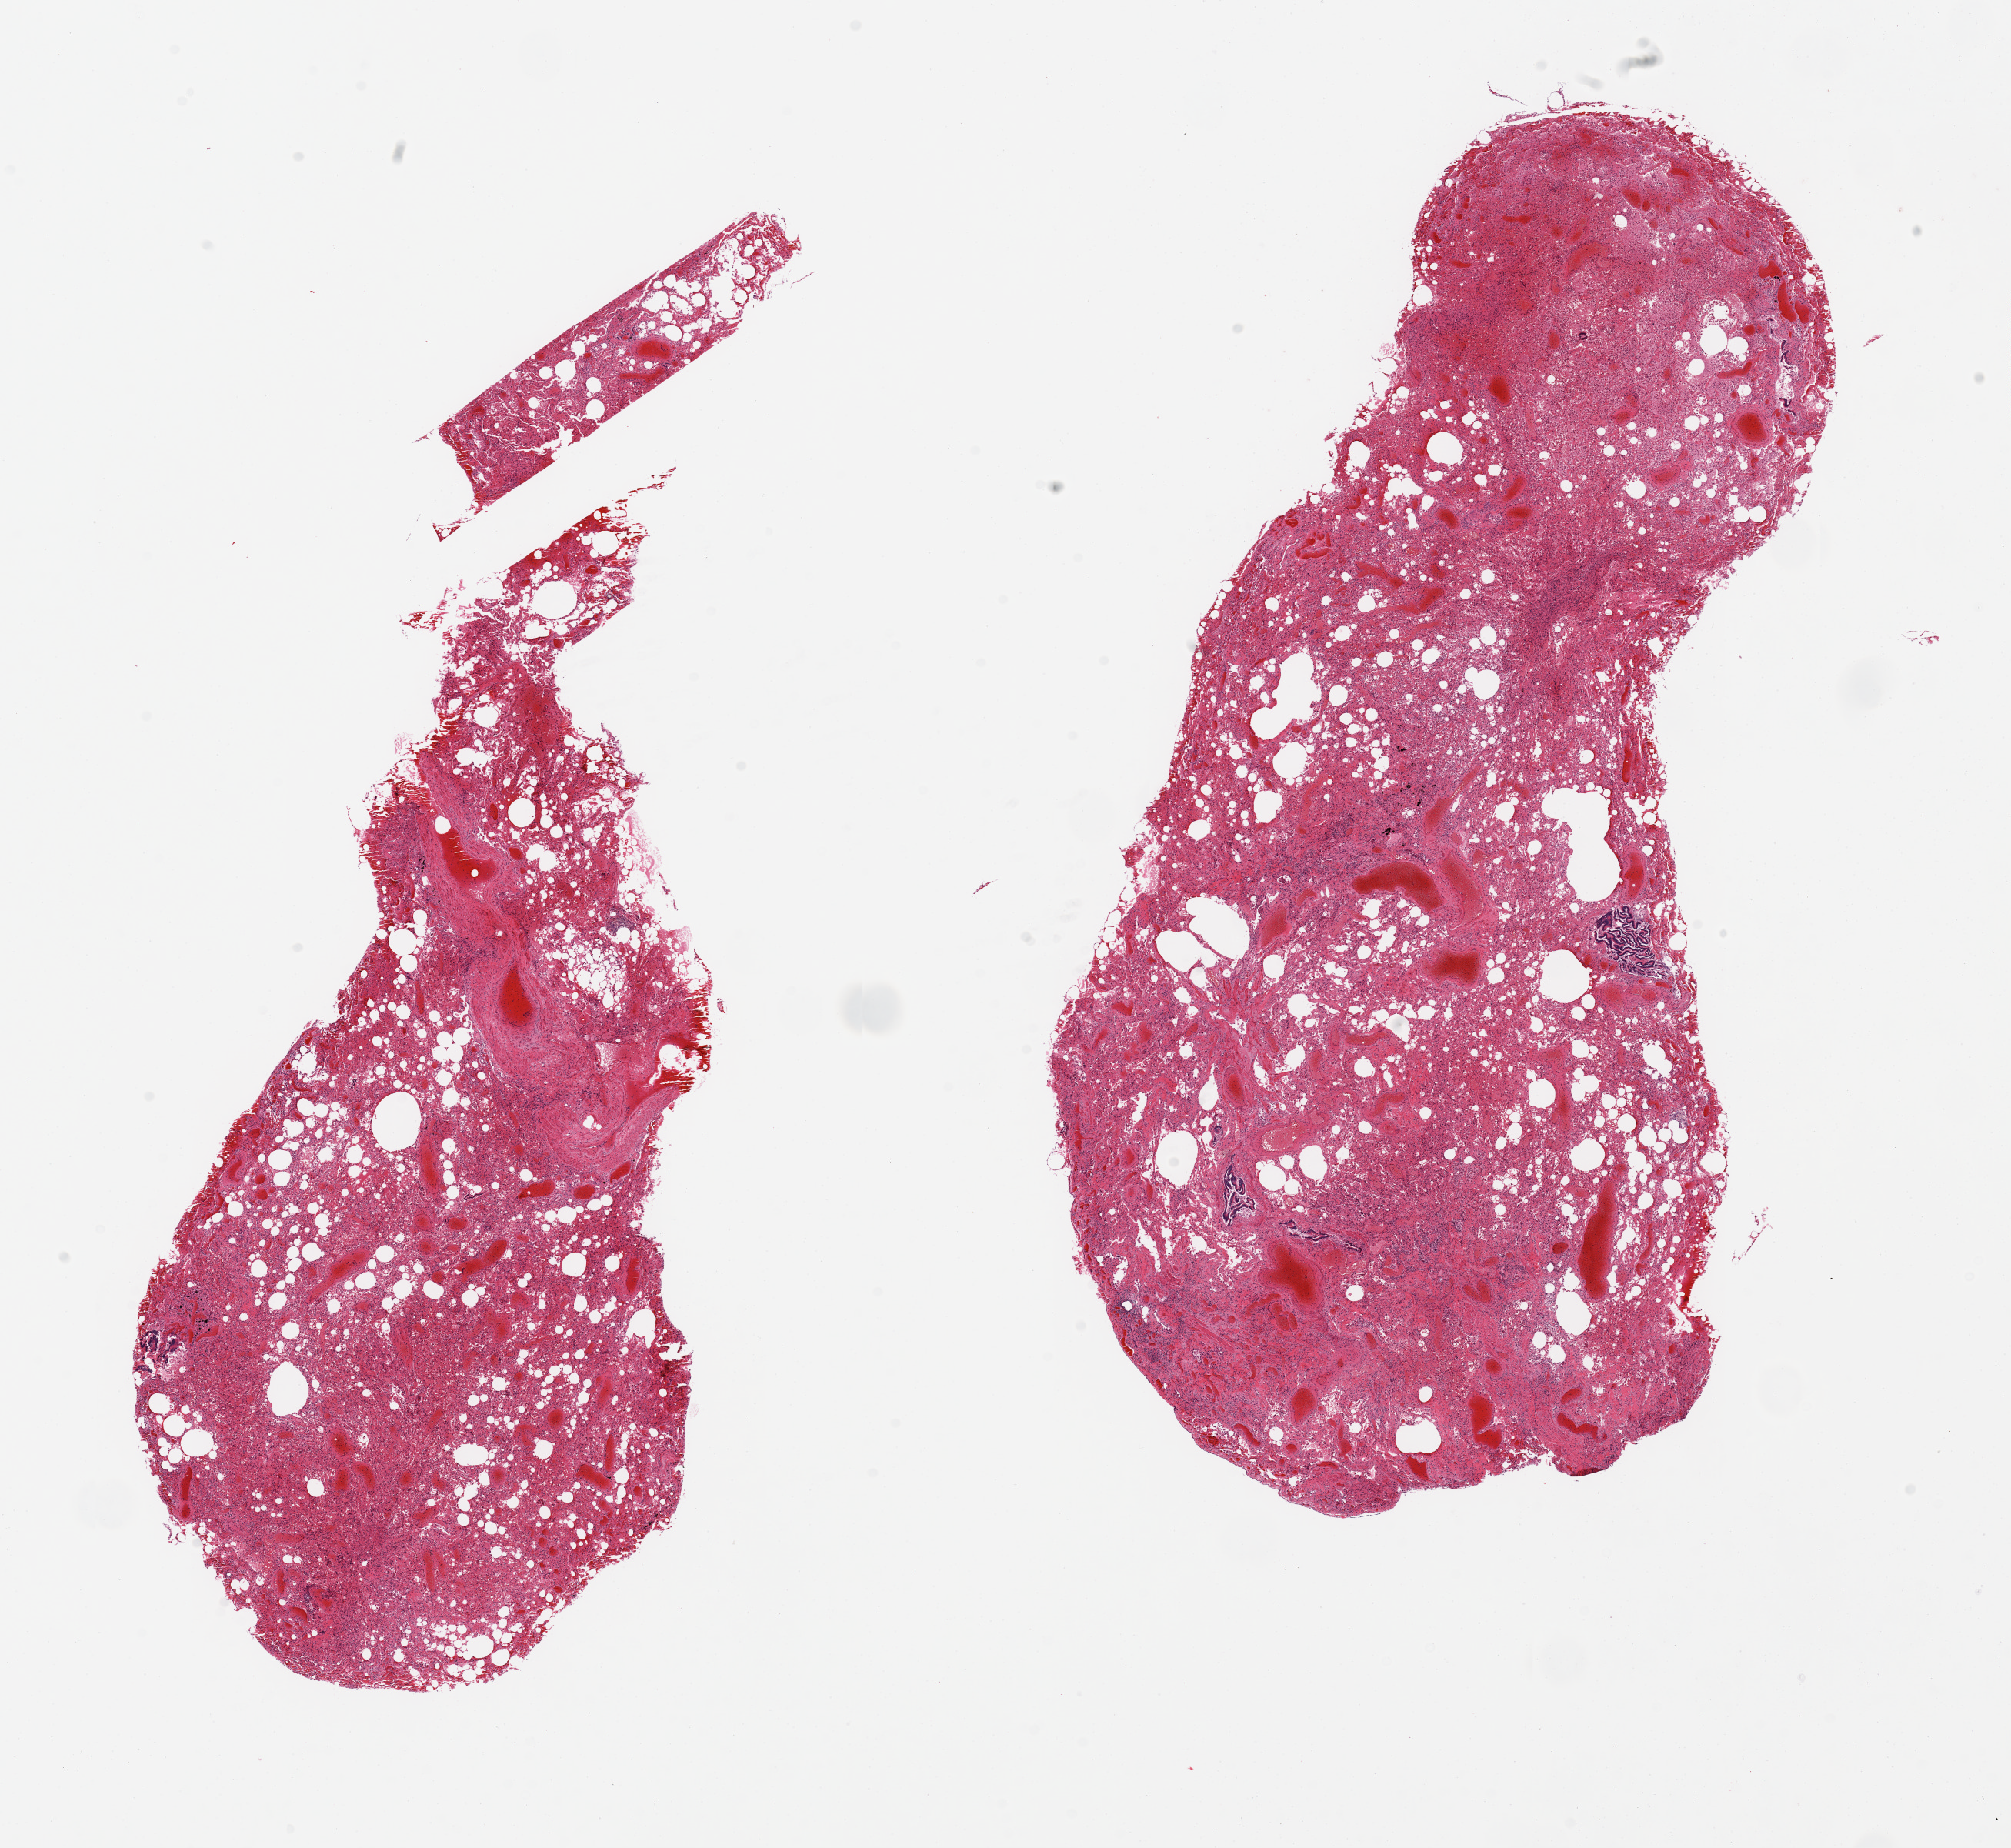
Haematoxylin and eosin whole-slide image, a low-resolution overview of the entire scanned area, about 20.7 x 19.0 mm (slide scanned at 20x). PAXgene-fixed paraffin-embedded (PFPE) section. Sampled site (target tissue): lung. Donor tissue sample. Donor: female.
Review note (as recorded): 2 pieces, diffuse moderate-marked acute/chronic pneumonitis/congestion.